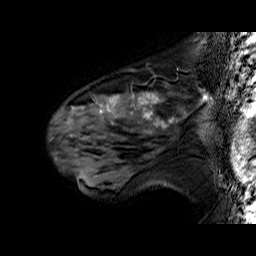
Breast MRI (dynamic contrast-enhanced), one sagittal slice. Dynamic contrast-enhanced series, time point 2 of 6 at this slice position (early post-contrast). 1.5 T. TE 6.4 ms, TR 32.9 ms. 4 mm slice thickness. 256 × 256 image matrix. Female patient. Case-level facts recorded for this patient, not image findings: setting: breast cancer imaged before/during neoadjuvant chemotherapy; receptor status: HER2-positive.
Outlined on this slice (semi-automatic segmentation, software-assisted and operator-edited):
- analysis volume of interest (the breast-tissue region the enhancement analysis was run in; not a lesion): bounding box [x1, y1, x2, y2] px = [51, 80, 196, 160]
- tumour enhancement mask (voxels above the 100 % enhancement threshold inside the analysis volume of interest): [72, 93, 172, 133]